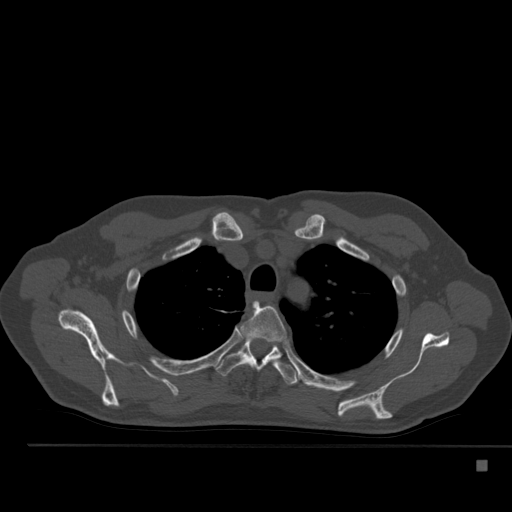
CT including the spine, one axial slice; position 389 of 517 along the scan axis; 120 kVp; bone window (W 1800 / L 400 HU); 512 × 512 image matrix. Male patient, age 70 years. From the clinical record (not read from this slice): primary cancer: renal; vertebrae with lytic lesions (as recorded): T4, T6, T10, T12, L3, L4, L5.
Structures marked on this image (semi-automatic segmentation, software-assisted and operator-edited):
- T3 vertebra: bounding box <241,301,287,342> (left, top, right, bottom; pixels)
- T4 vertebra: <215,338,301,385>